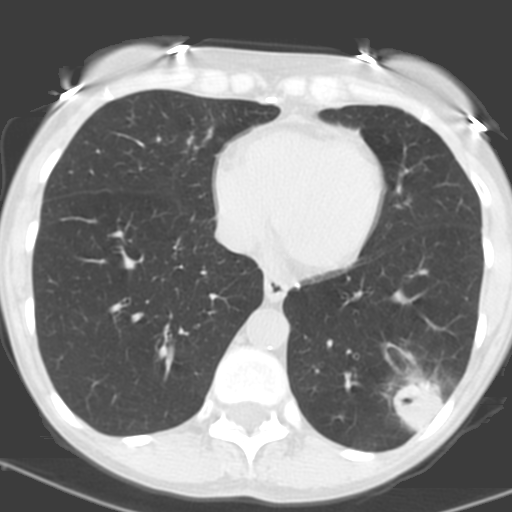
Low-dose screening chest CT, one axial slice; slice 55 of 156 in the series (ordered by position); 120 kVp; lung window (W 1500 / L -600 HU); 3.2 mm slice thickness; 512 × 512 image matrix, field of view 262 × 262 mm.
Outlined on this slice (expert manual segmentation):
- lesion 1 (tumor, lower lobe of left lung): bounding box <392,375,442,432> (left, top, right, bottom; pixels)